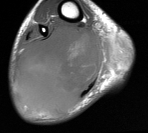
MRI of an extremity soft-tissue mass, one axial slice; slice 34 of 76 in the series (ordered by position); MR volume resampled by the dataset authors to the PET/CT grid (not the native acquisition matrix); 3.27 mm slice thickness; 148 × 133 image matrix. Male patient. Case-level facts recorded for this patient, not image findings: histological type: liposarcoma - round cell; grade: high; site of the primary tumour: right calf.
Outlined on this slice (expert contour drawn on MRI and transferred to this co-registered scan by the dataset authors):
- gross tumour volume (mass): bounding box <15,23,128,115> (left, top, right, bottom; pixels)